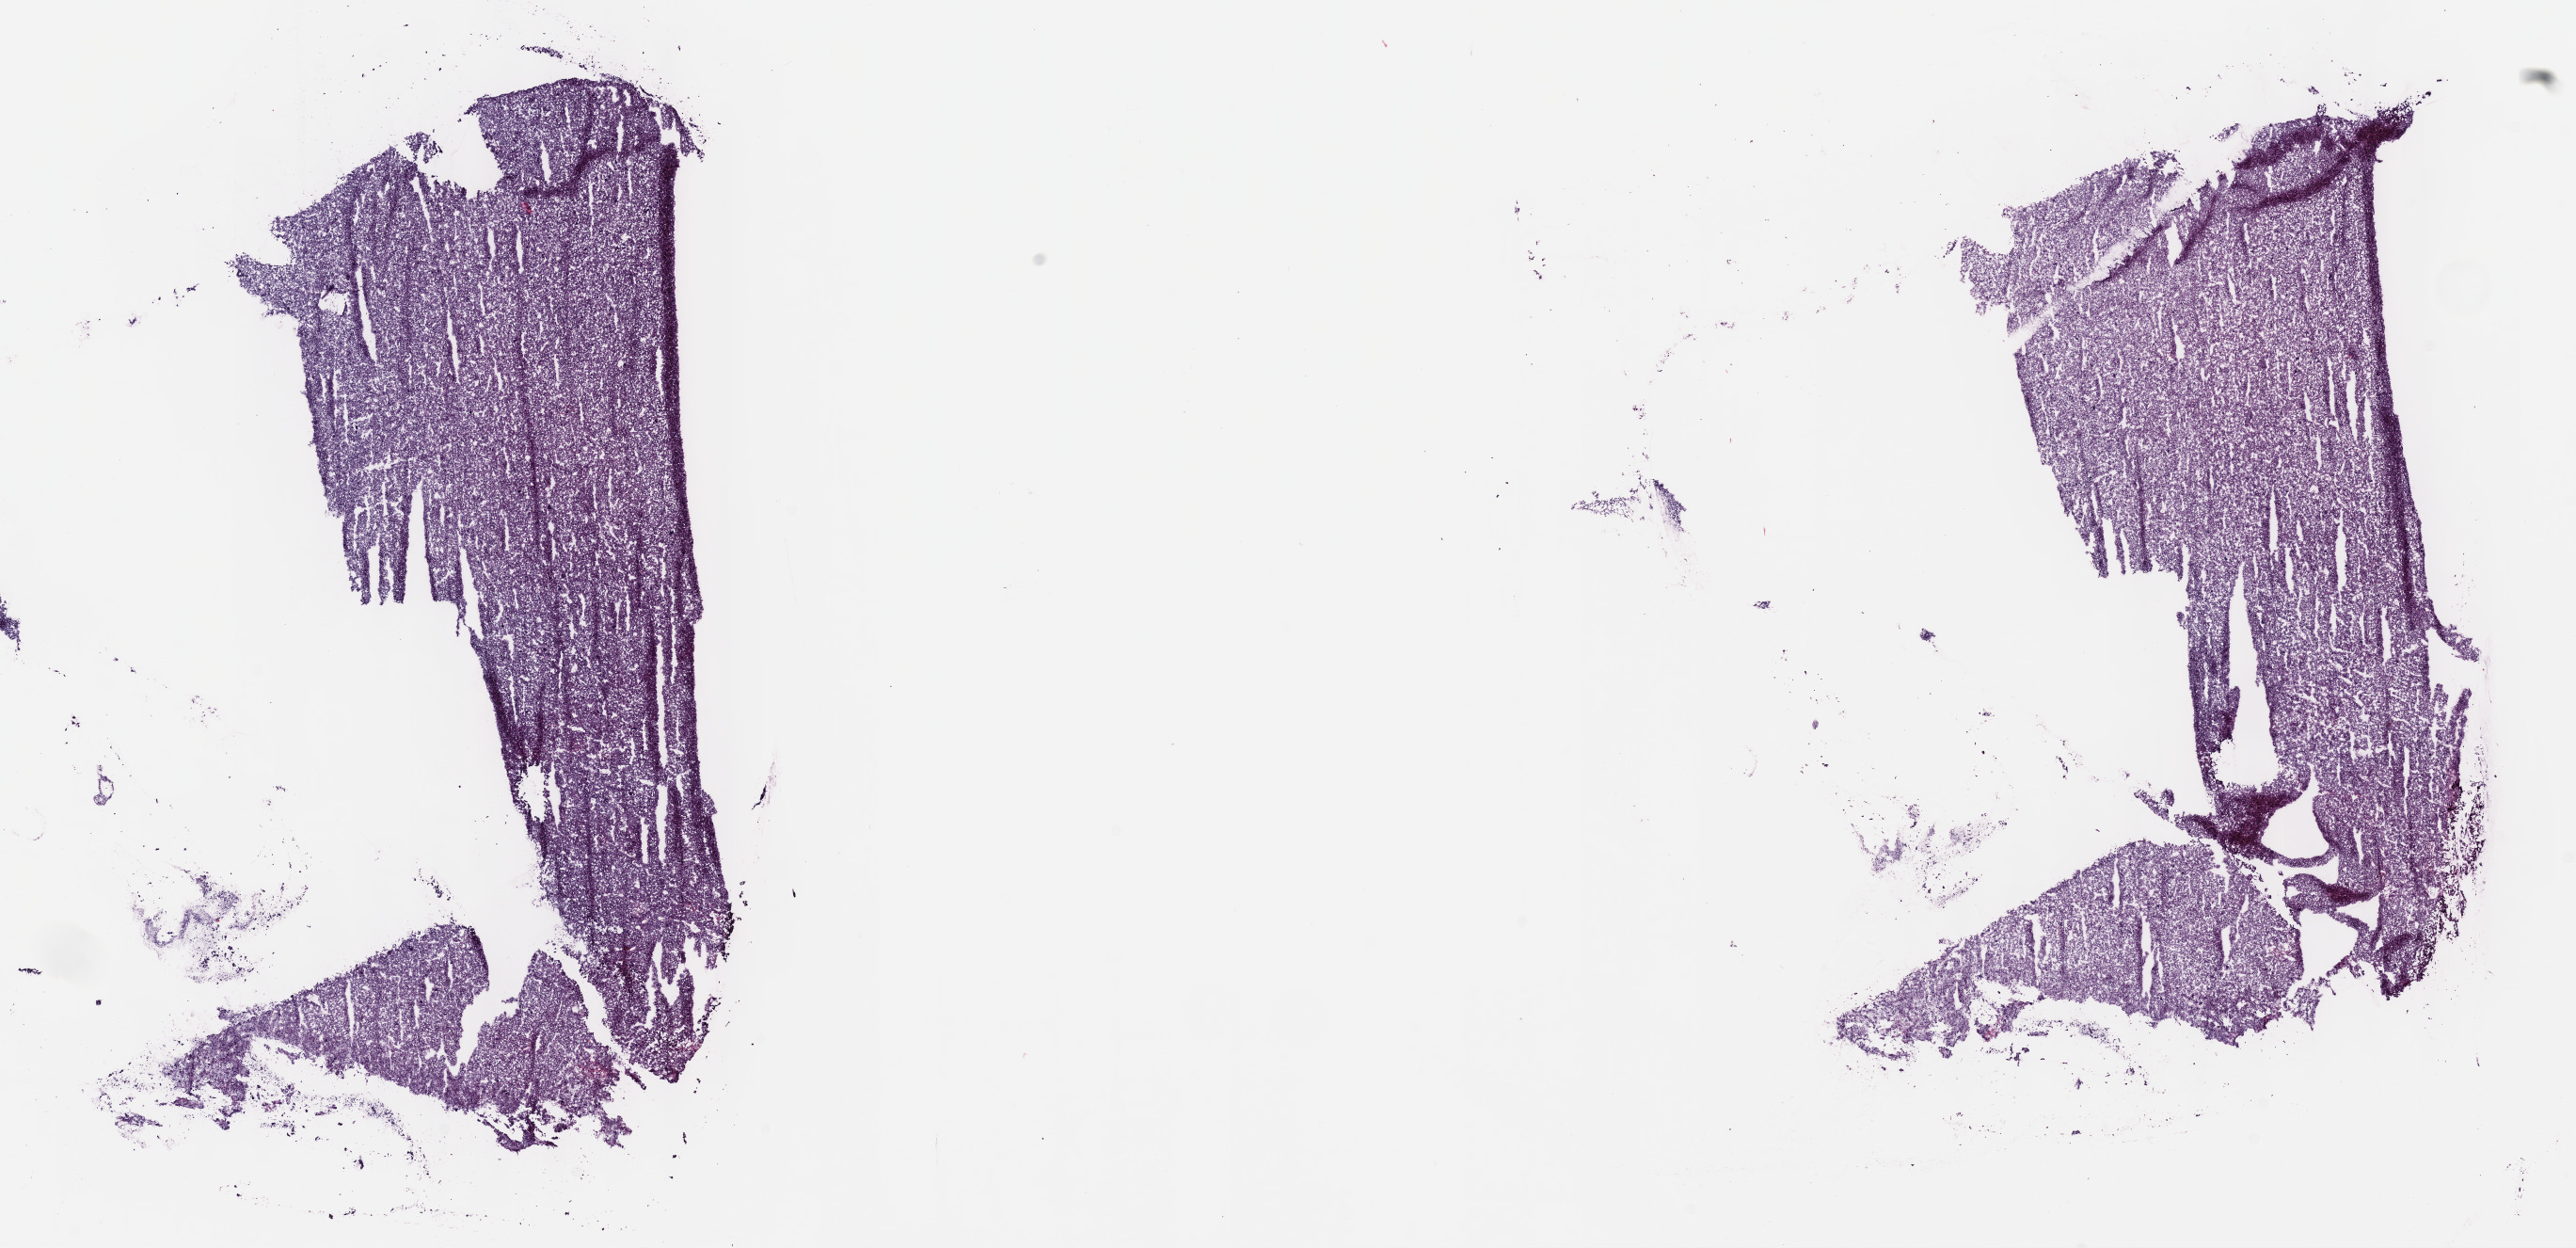
Whole-slide histology image, H&E, a low-resolution overview of the entire scanned area, about 22.1 x 10.7 mm (acquisition: 40x scan), frozen section from the top of the tissue portion, liver, primary tumour sample. Male patient; age at initial diagnosis 48 years. Histologic grade: G2 (moderately differentiated). Composition of this section per pathologist review: tumour cells 90%, tumour nuclei 95%, normal cells 0%, stromal cells 0%, necrosis 10%. Infiltration values recorded for this section: lymphocyte infiltration 0%, monocyte infiltration 0%, neutrophil infiltration 0%.
- AJCC pathologic stage: II
- pathologic diagnosis: Hepatocellular carcinoma, NOS